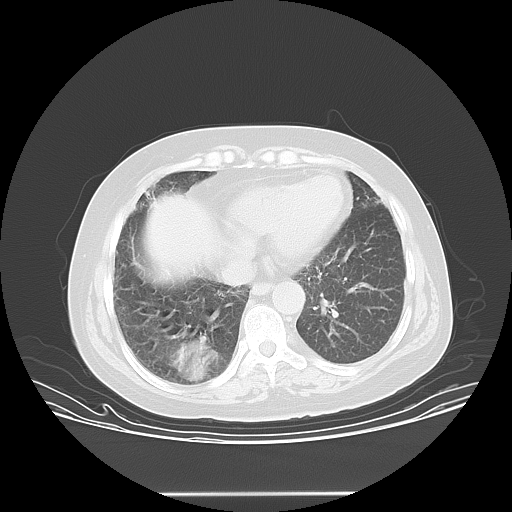
Chest CT, one axial slice; slice 11 of 45 in the series (ordered by position); reconstruction kernel LUNG; lung window (W 1500 / L -600 HU); 512 × 512 image matrix, field of view 408 × 408 mm. Female patient, age 55 years. From the clinical record (not read from this slice): clinical TNM (as recorded): T2 N0 M1b.
Outlined on this slice (bounding box drawn by a radiologist):
- lung tumour (recorded histology: squamous cell carcinoma): bounding box <157,336,215,385> (left, top, right, bottom; pixels)